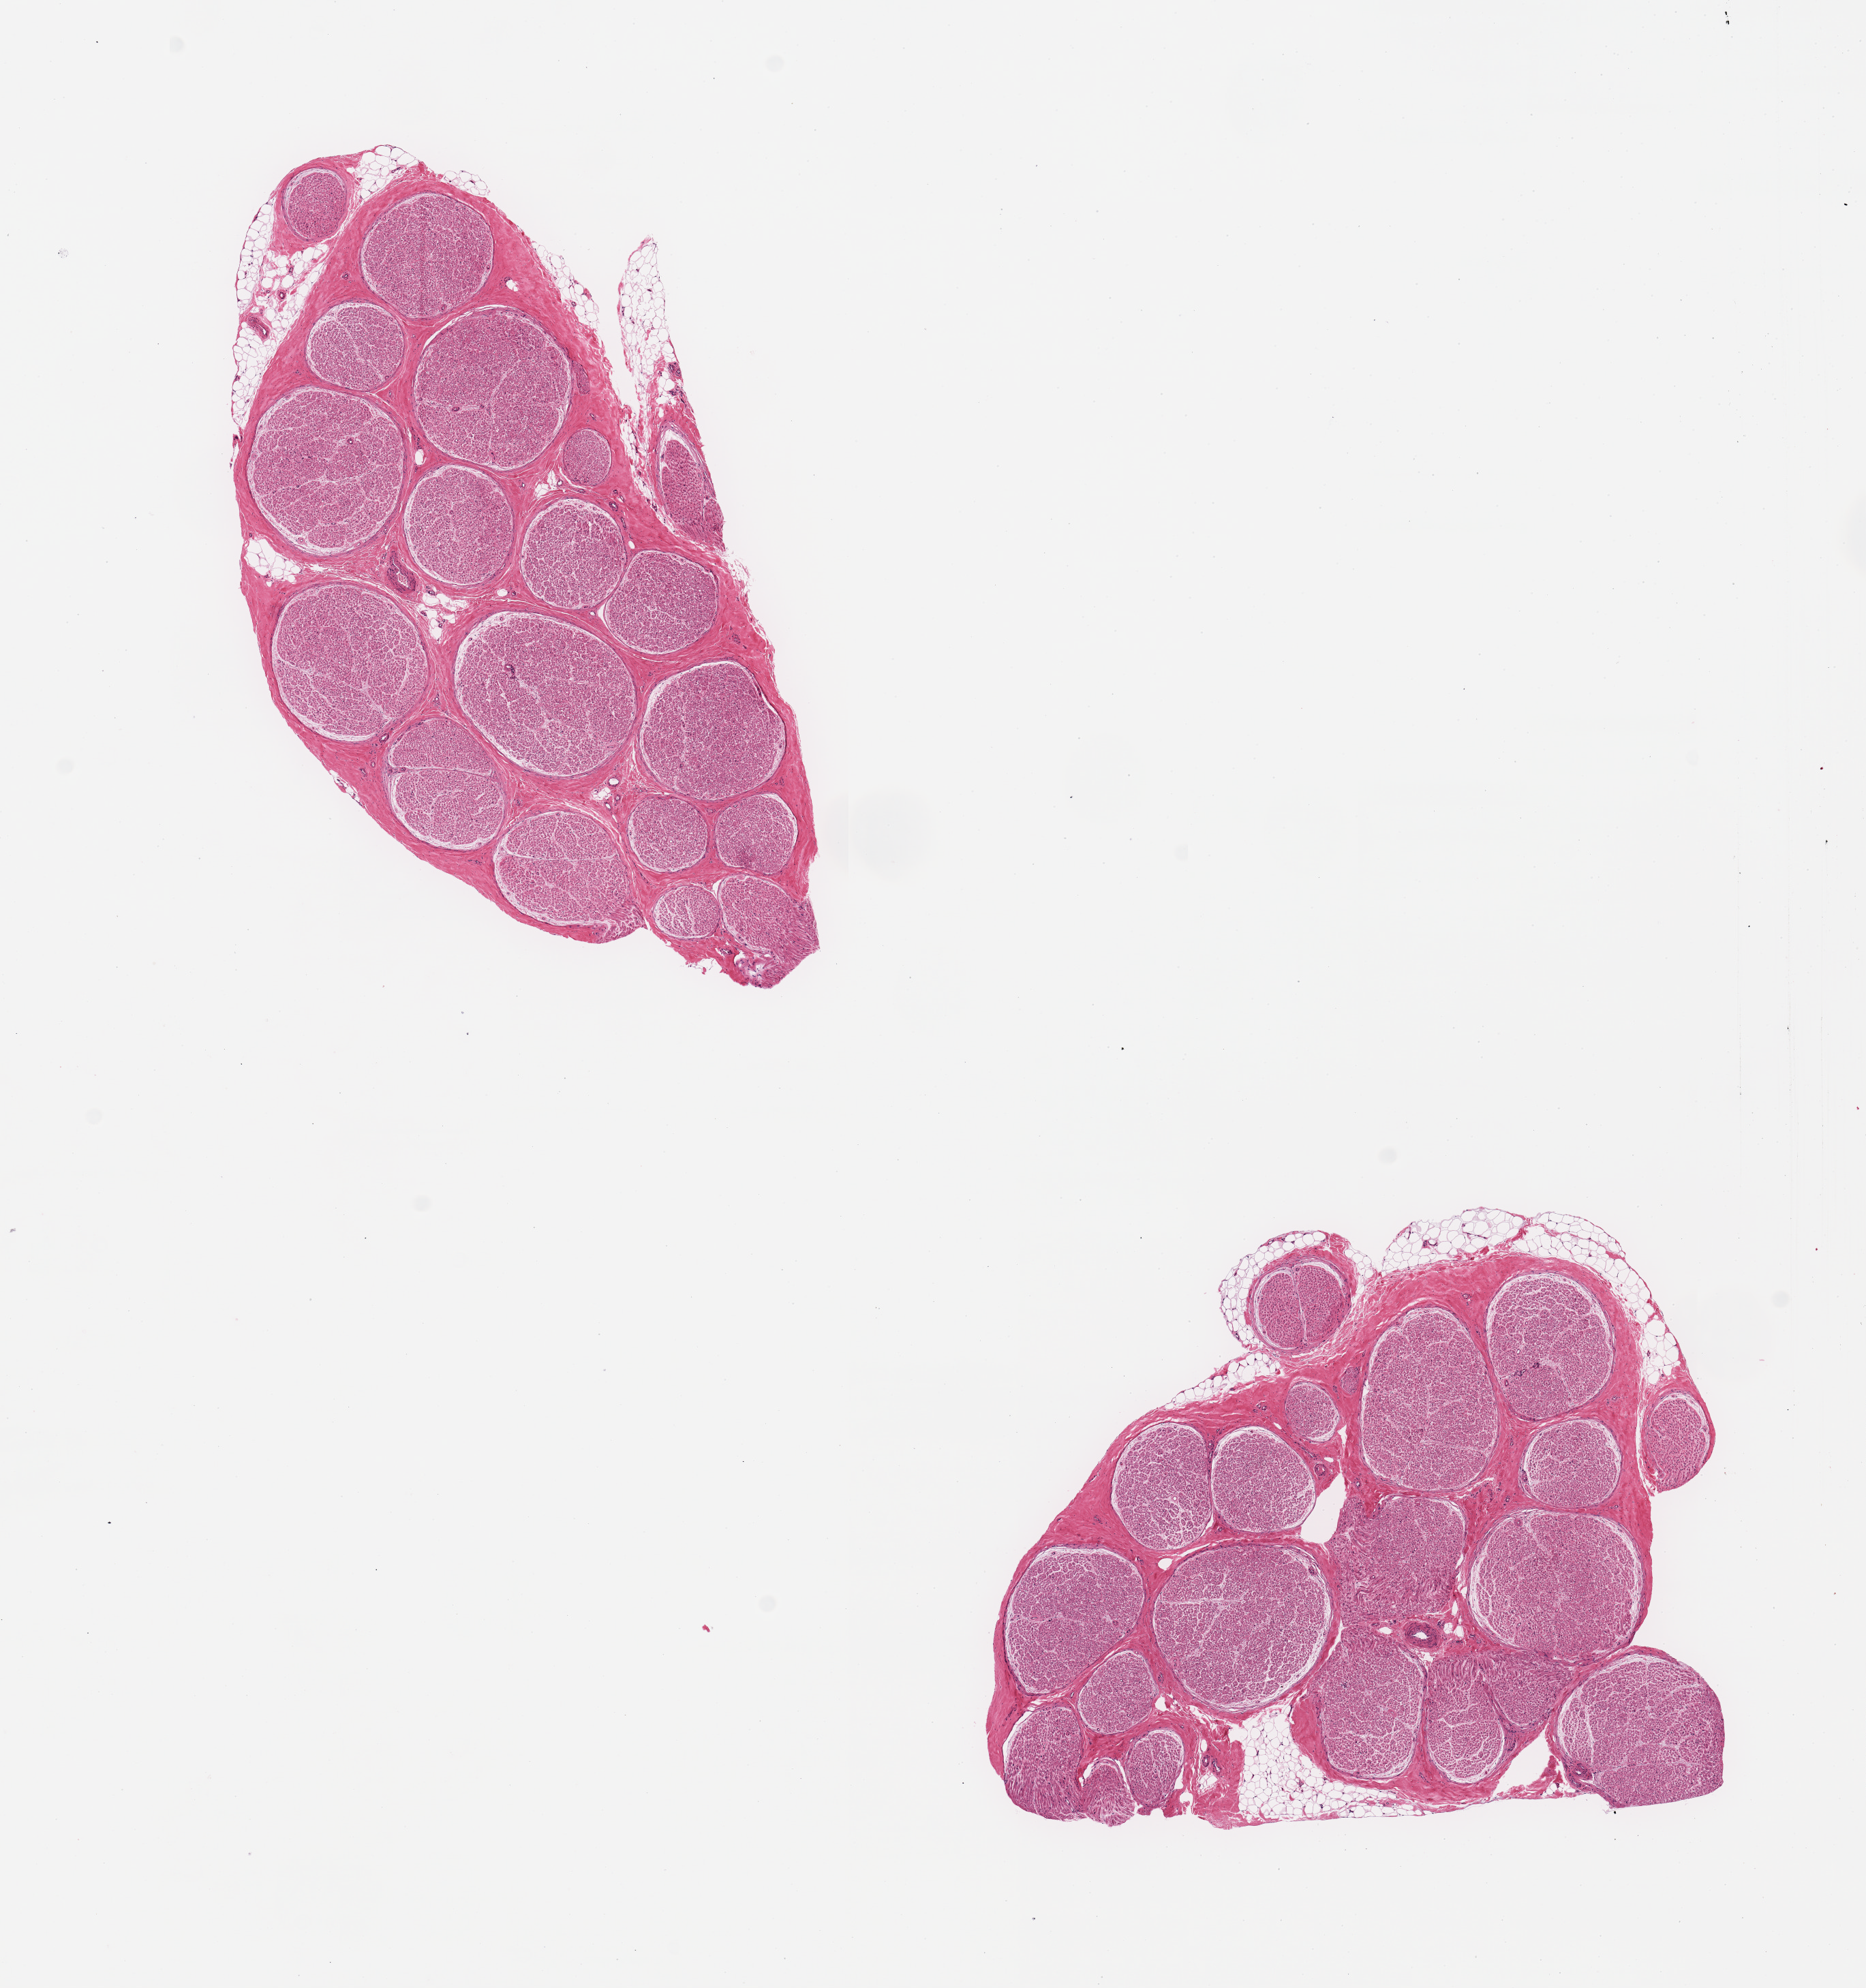
Whole-slide image, hematoxylin and eosin (H&E) stain, brightfield, shown as a low-resolution overview of the whole scanned area (about 10.8 x 11.5 mm, from a 20x scan), PAXgene-fixed, paraffin-embedded tissue, target tissue: tibial nerve, donor tissue sample. Female donor.
• reviewer comment on this tissue sample: 2 pieces, trace adherent fat